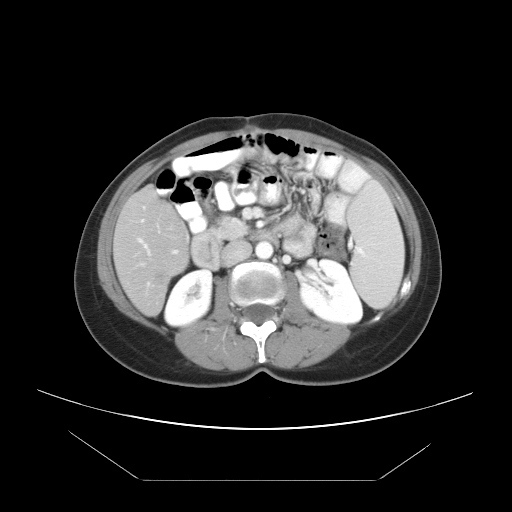
Contrast-enhanced abdominal CT, one axial slice; position 16 of 45 along the scan axis; intravenous contrast given; soft-tissue window (W 400 / L 40 HU); 5 mm slice thickness; 512 × 512 image matrix, field of view 405 × 405 mm. Female patient, age 52 years. From the clinical record (not read from this slice): diagnosis: colorectal cancer liver metastases, imaged before liver resection; multiple liver metastases: yes; largest metastasis: 2.5 cm; disease in both lobes: no.
Annotated regions visible in this slice (outlined manually by an expert reader):
- hepatic veins: bounding box (x1, y1, x2, y2) in pixels: (139, 239, 150, 284)
- liver: (116, 189, 187, 314)
- planned liver remnant (the part of the liver to remain after resection): (116, 189, 187, 248)
- portal vein (with intrahepatic branches): (140, 219, 178, 266)
- liver metastasis: (154, 273, 164, 288)